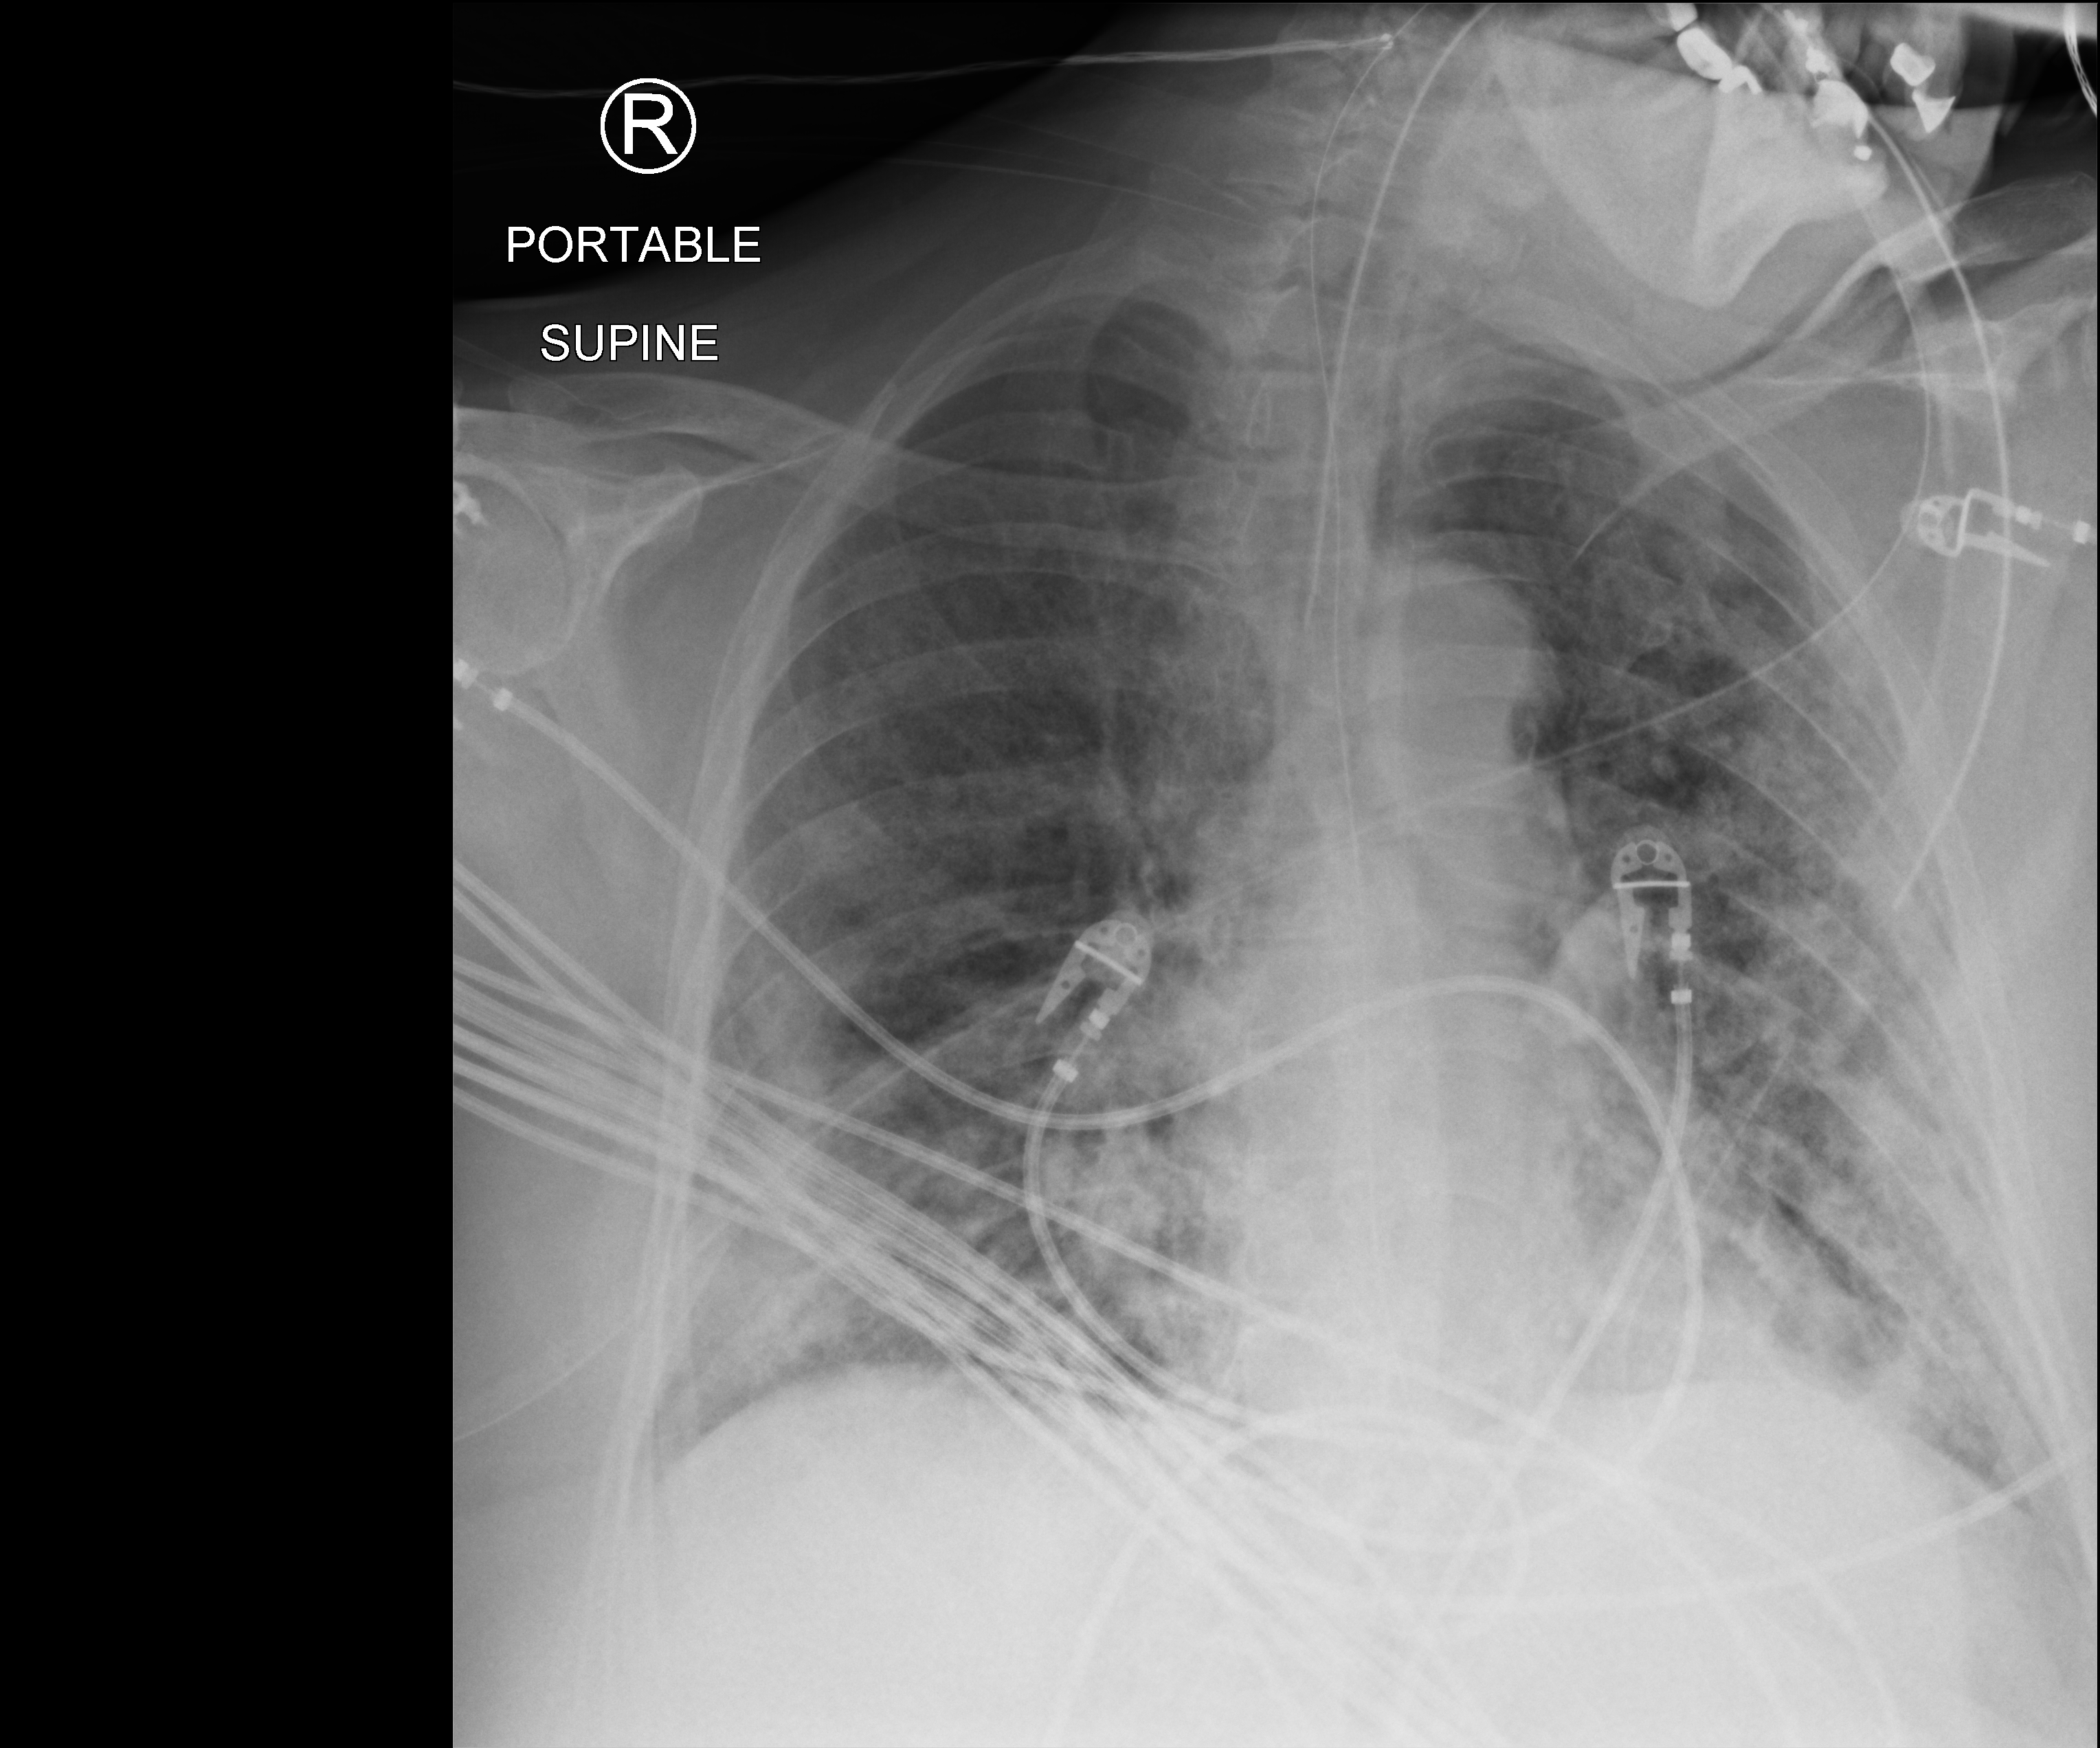
Portable chest radiograph. Female patient hospitalised with COVID-19, age 60–74 years.
From the hospital-stay record, not from the radiograph (when in the stay this image was taken is not recorded):
- mechanically ventilated during this hospital stay: yes